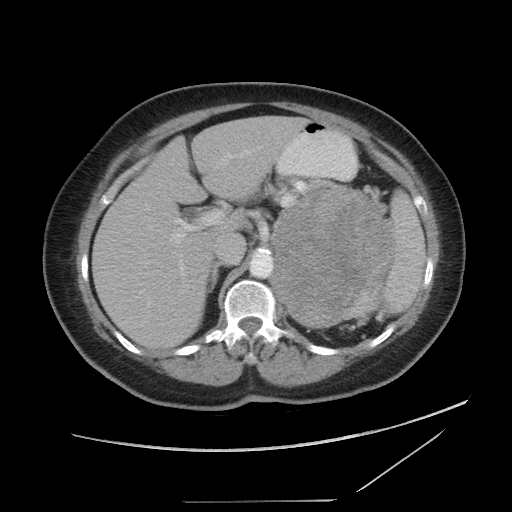
Contrast-enhanced abdominal CT, one axial slice. Position 60 of 86 along the scan axis. 120 kVp. Intravenous contrast given. Soft-tissue window (W 400 / L 40 HU). 5 mm slice thickness. 512 × 512 image matrix, field of view 398 × 398 mm. Patient: female, 77 years. Case-level facts recorded for this patient, not image findings: diagnosis: adrenocortical carcinoma; tumour side: left adrenal; tumour size at pathology: 13.1 cm; Ki-67 index: 10 %; stage (as recorded): 3.
Outlined on this slice (semi-automatic segmentation, software-assisted and operator-edited):
- mass: bounding box (x1, y1, x2, y2) in pixels: (273, 191, 394, 327)